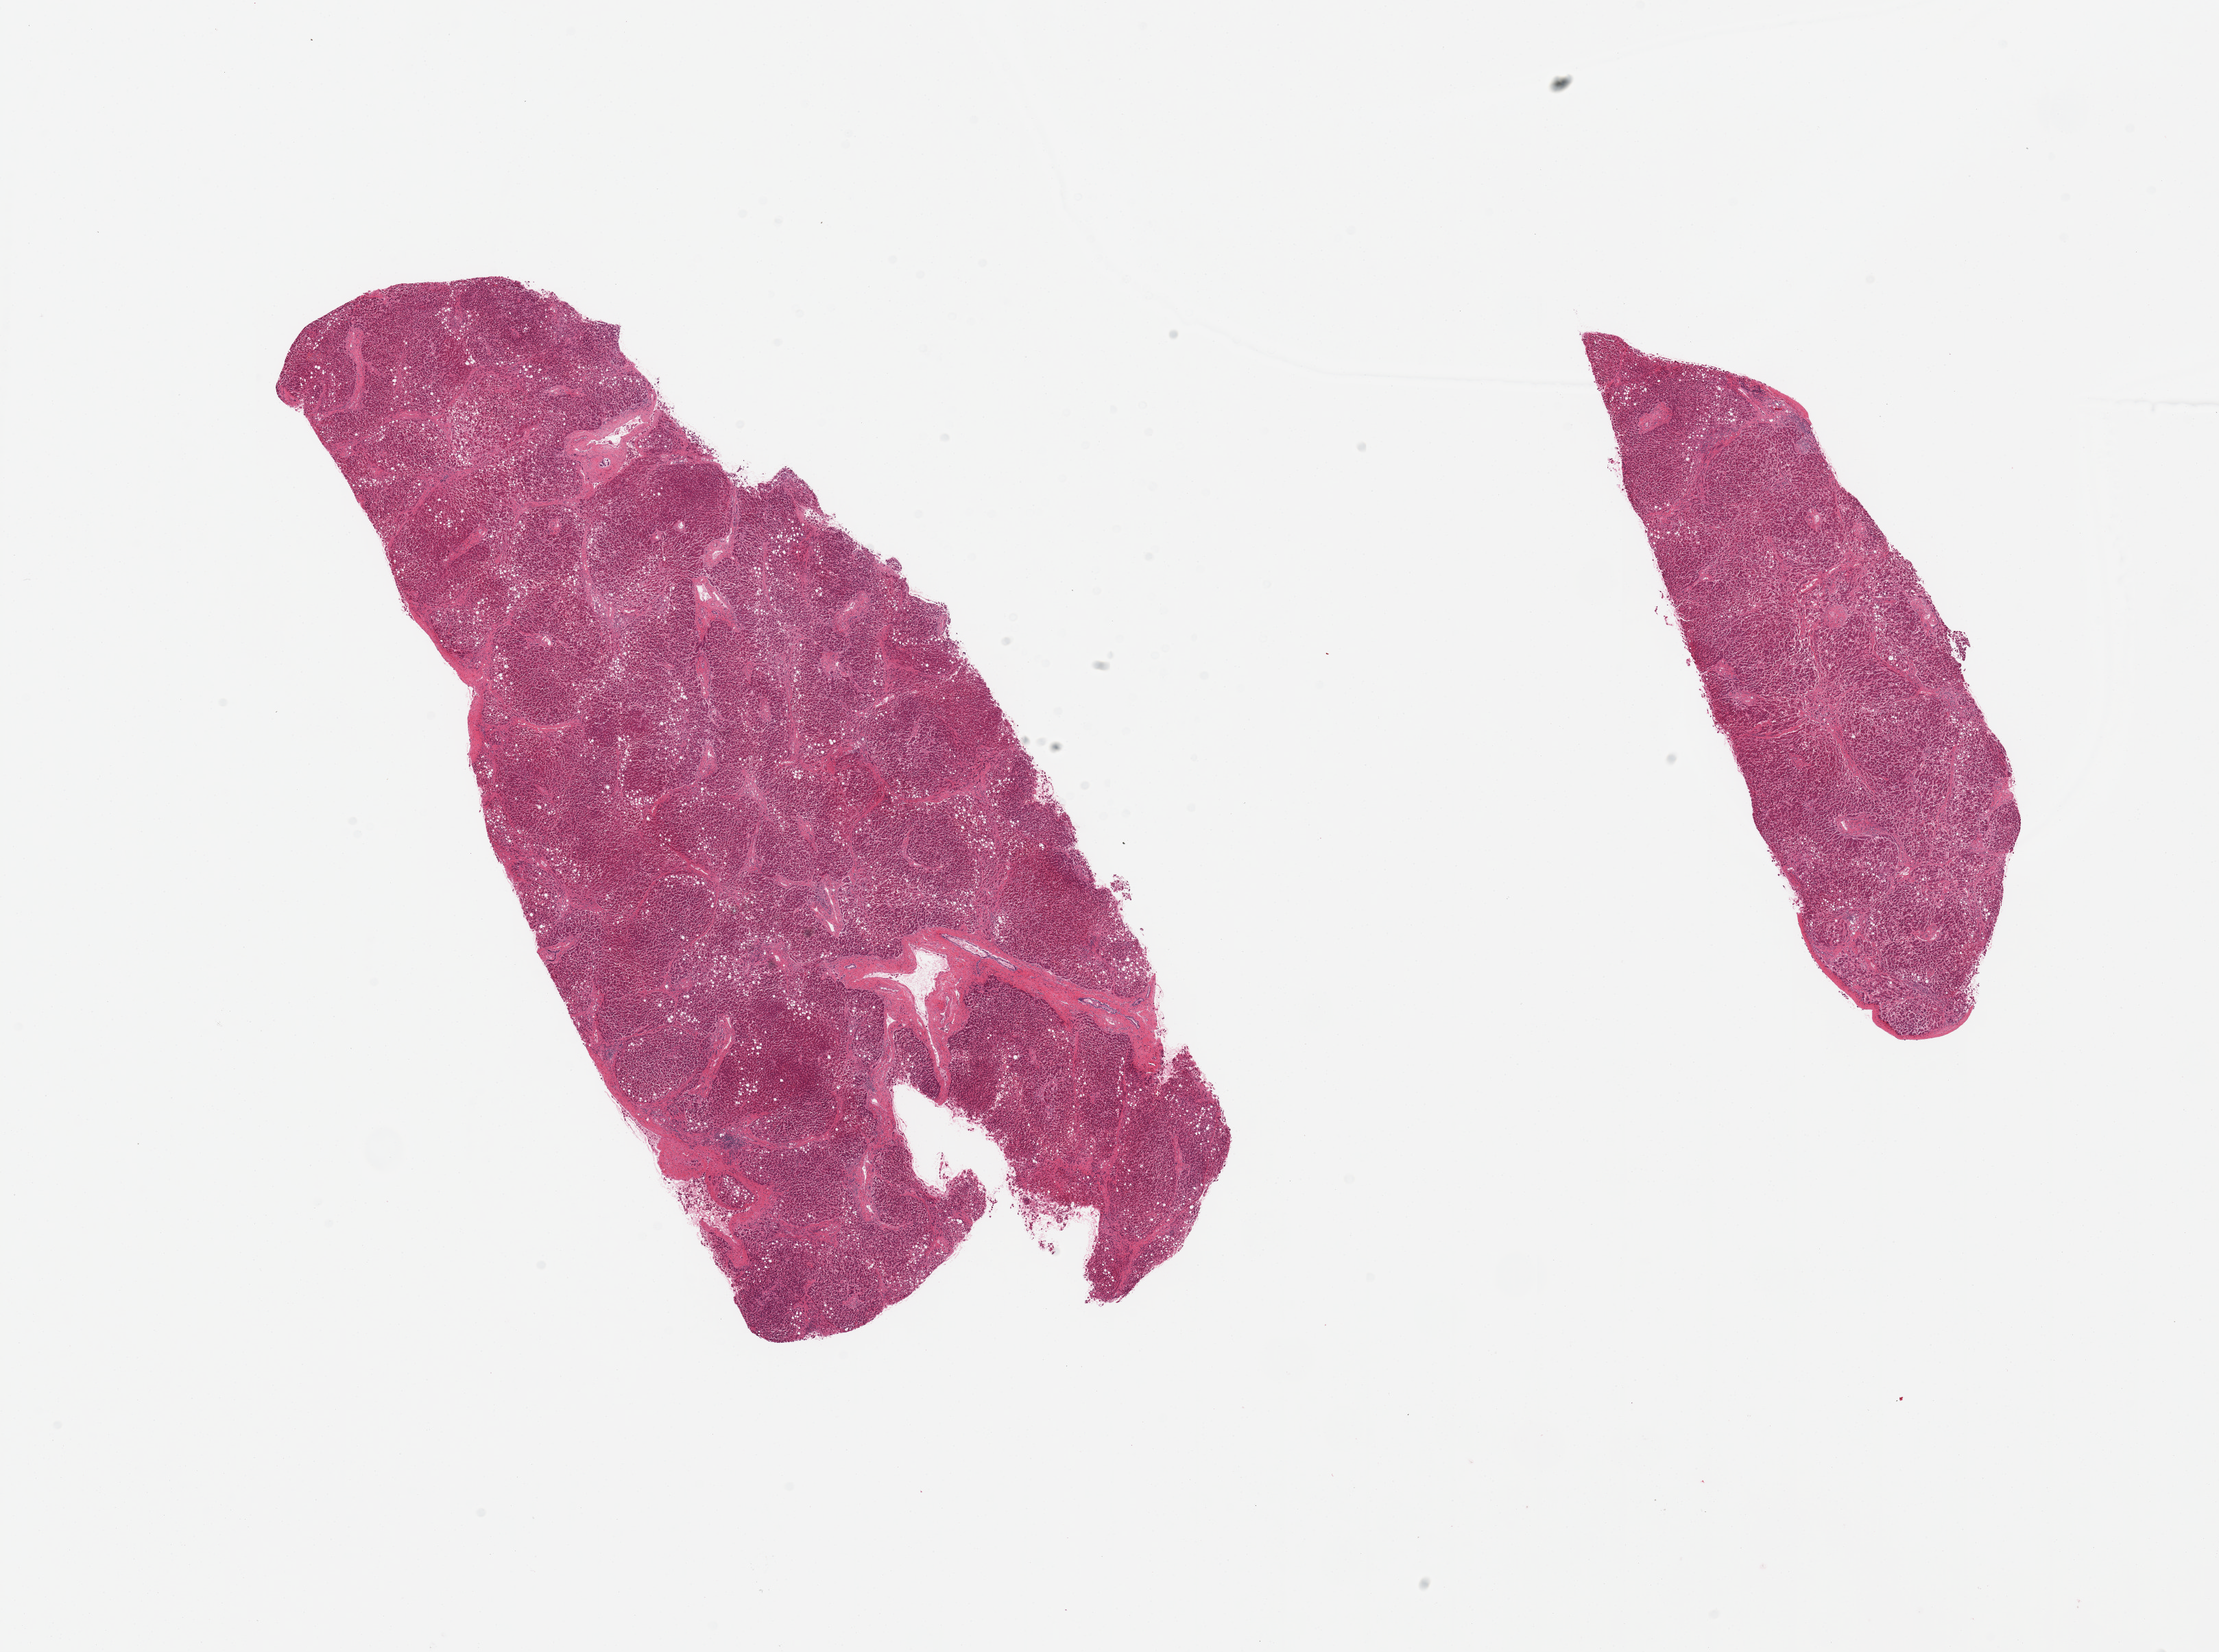
Hematoxylin and eosin (H&E) whole-slide image, low-resolution overview of the scanned area, about 25.6 x 19.1 mm (from a 20x scan); PAXgene-fixed, paraffin-embedded tissue; section of liver (target tissue); donor tissue sample.
Review note (as recorded): 2 pieces, moderate steatosis, bridging fibrosis.